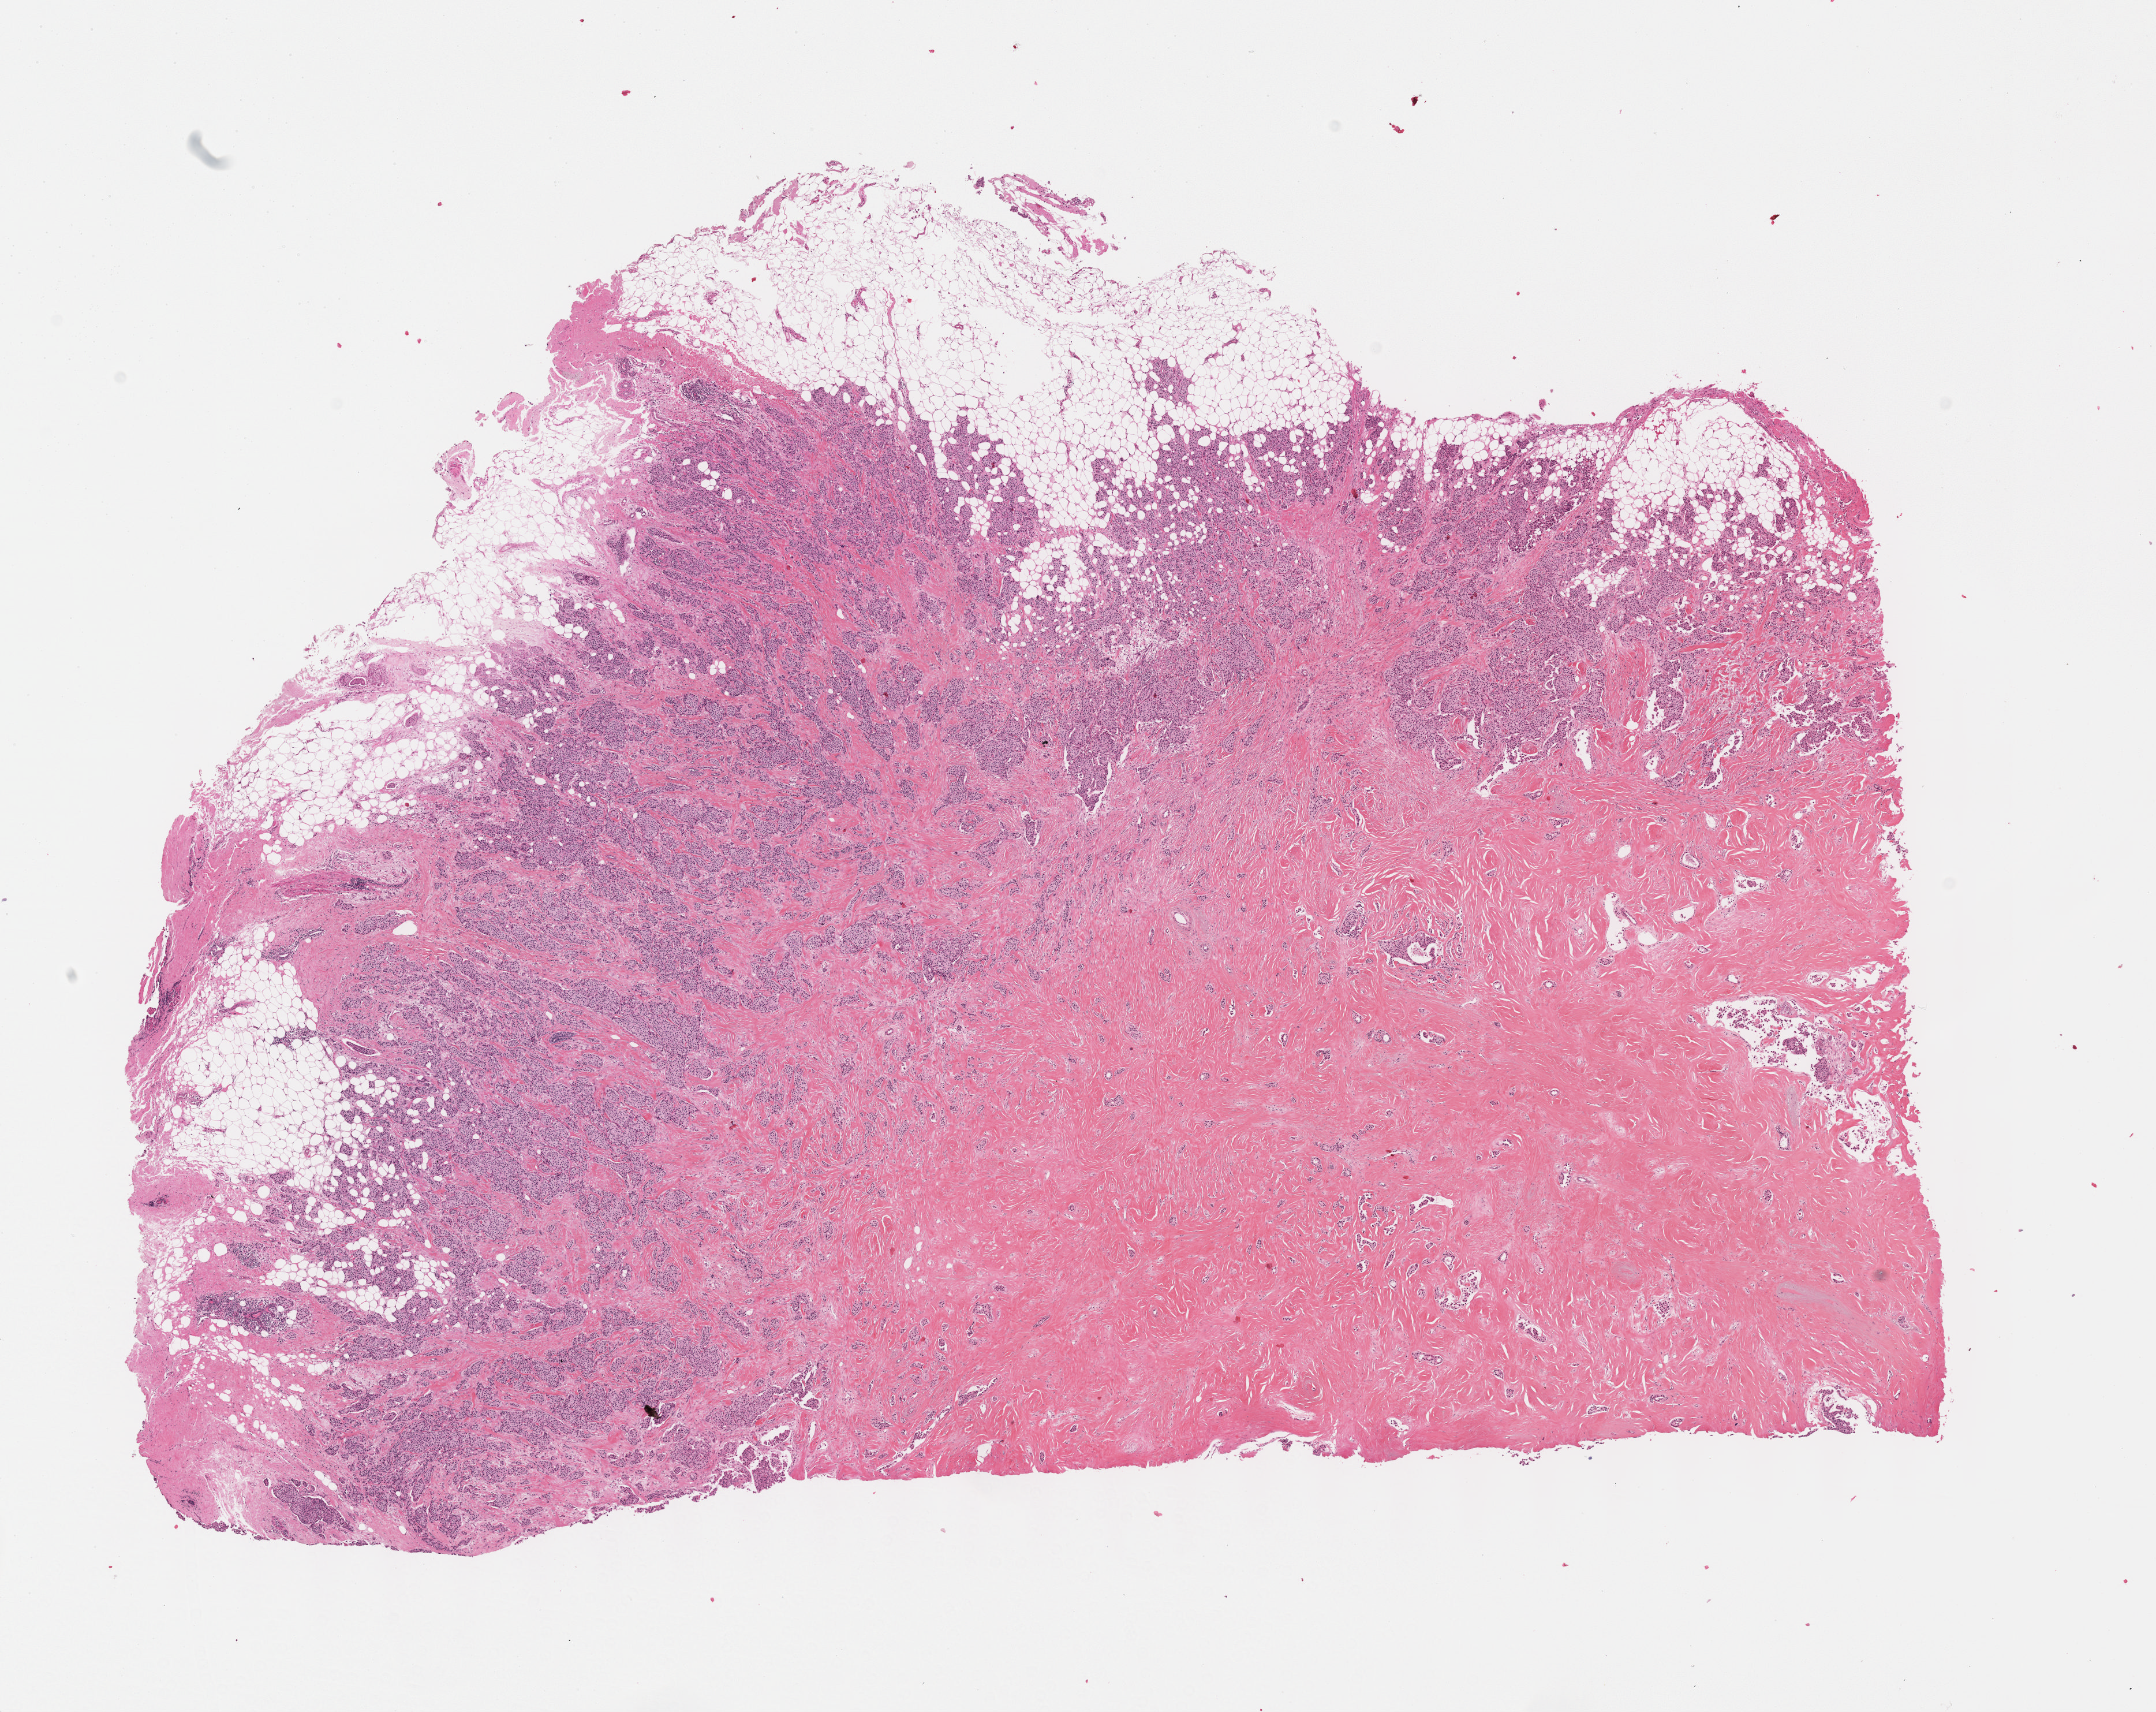
Digitized H&E-stained tissue section (whole slide), a low-resolution overview of the entire scanned area, about 15.1 x 12.0 mm; FFPE section; breast, primary tumour sample. Patient: female, age at initial diagnosis 69 years.
- lymph nodes positive (case pathology): 1 of 19 examined
- AJCC pathologic stage: IIIA
- pathologic diagnosis: Infiltrating duct carcinoma, NOS